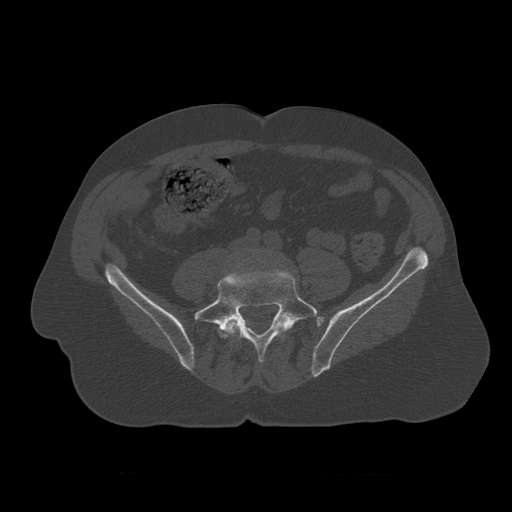
CT including the spine, one axial slice; slice 259 of 450 in the series (ordered by position); reconstruction kernel STANDARD; bone window (W 1800 / L 400 HU); 512 × 512 image matrix, field of view 405 × 405 mm. Patient age 75 years. Case-level facts recorded for this patient, not image findings: primary cancer: prostate.
Outlined on this slice (semi-automatically segmented with operator editing):
- L4 vertebra: bounding box (x1, y1, x2, y2) in pixels: (223, 319, 293, 338)
- L5 vertebra: (194, 269, 318, 363)